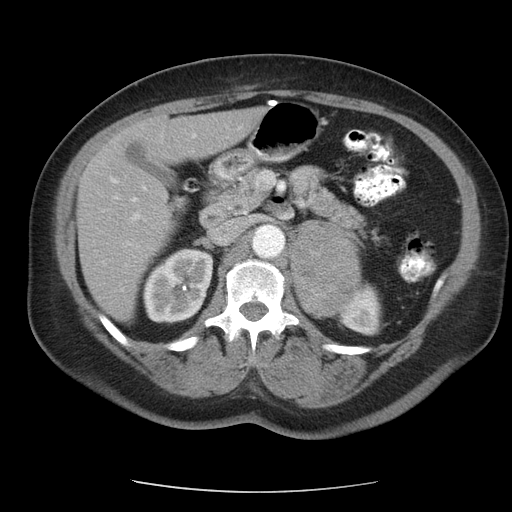
Contrast-enhanced abdominal CT, one axial slice. Slice 64 of 95 in the series (ordered by position). Intravenous contrast given. Soft-tissue window (W 400 / L 40 HU). 5 mm slice thickness. 512 × 512 image matrix, field of view 362 × 362 mm. Female patient, age 71 years. From the clinical record (not read from this slice): diagnosis: adrenocortical carcinoma; tumour side: left adrenal; tumour size at pathology: 8.8 cm; Ki-67 index: 20 %; stage (as recorded): 2.
Structures marked on this image (semi-automatic segmentation, software-assisted and operator-edited):
- mass: bounding box <292,221,360,315> (left, top, right, bottom; pixels)